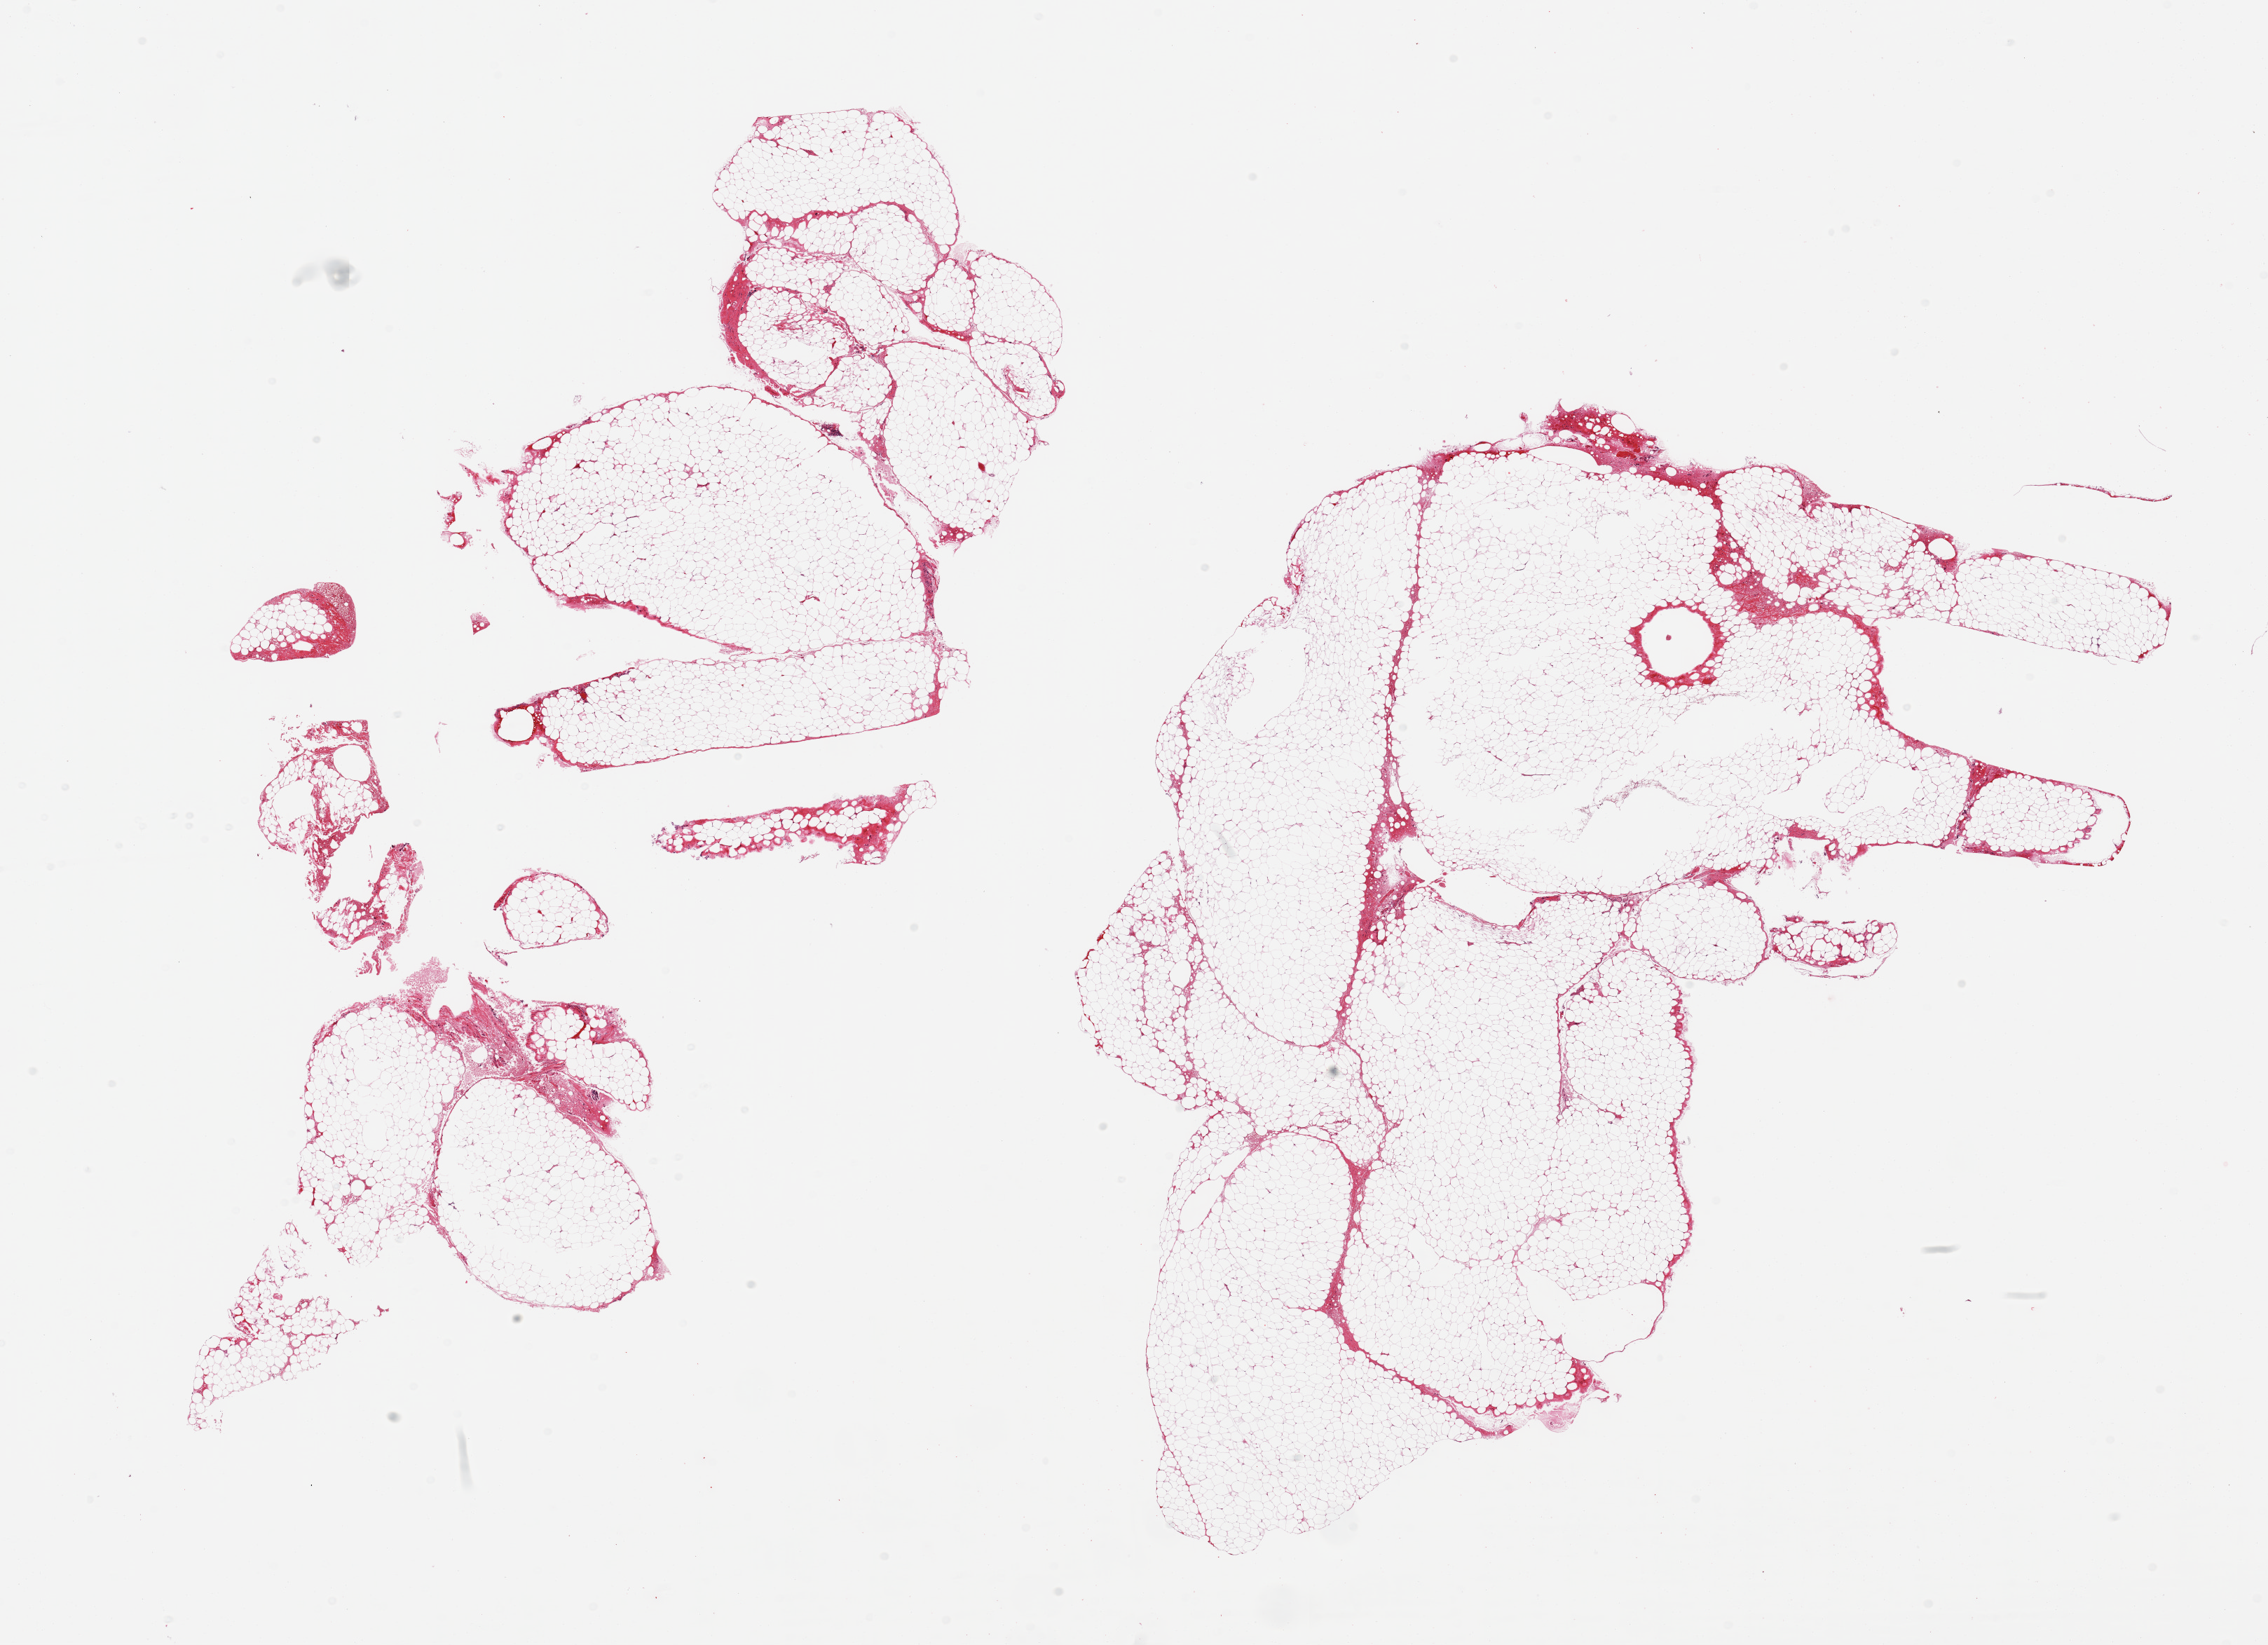
Whole-slide image, H&E stain — a low-resolution overview of the entire scanned area, about 25.6 x 18.6 mm (acquisition: 20x scan); PAXgene-fixed, paraffin-embedded tissue; target tissue: omentum; donor tissue sample. Male donor.
Reviewer comment on this tissue sample: 2 pieces, !0-15% is interstitial fascia/mesothelial hyperplasia/vascular elements.